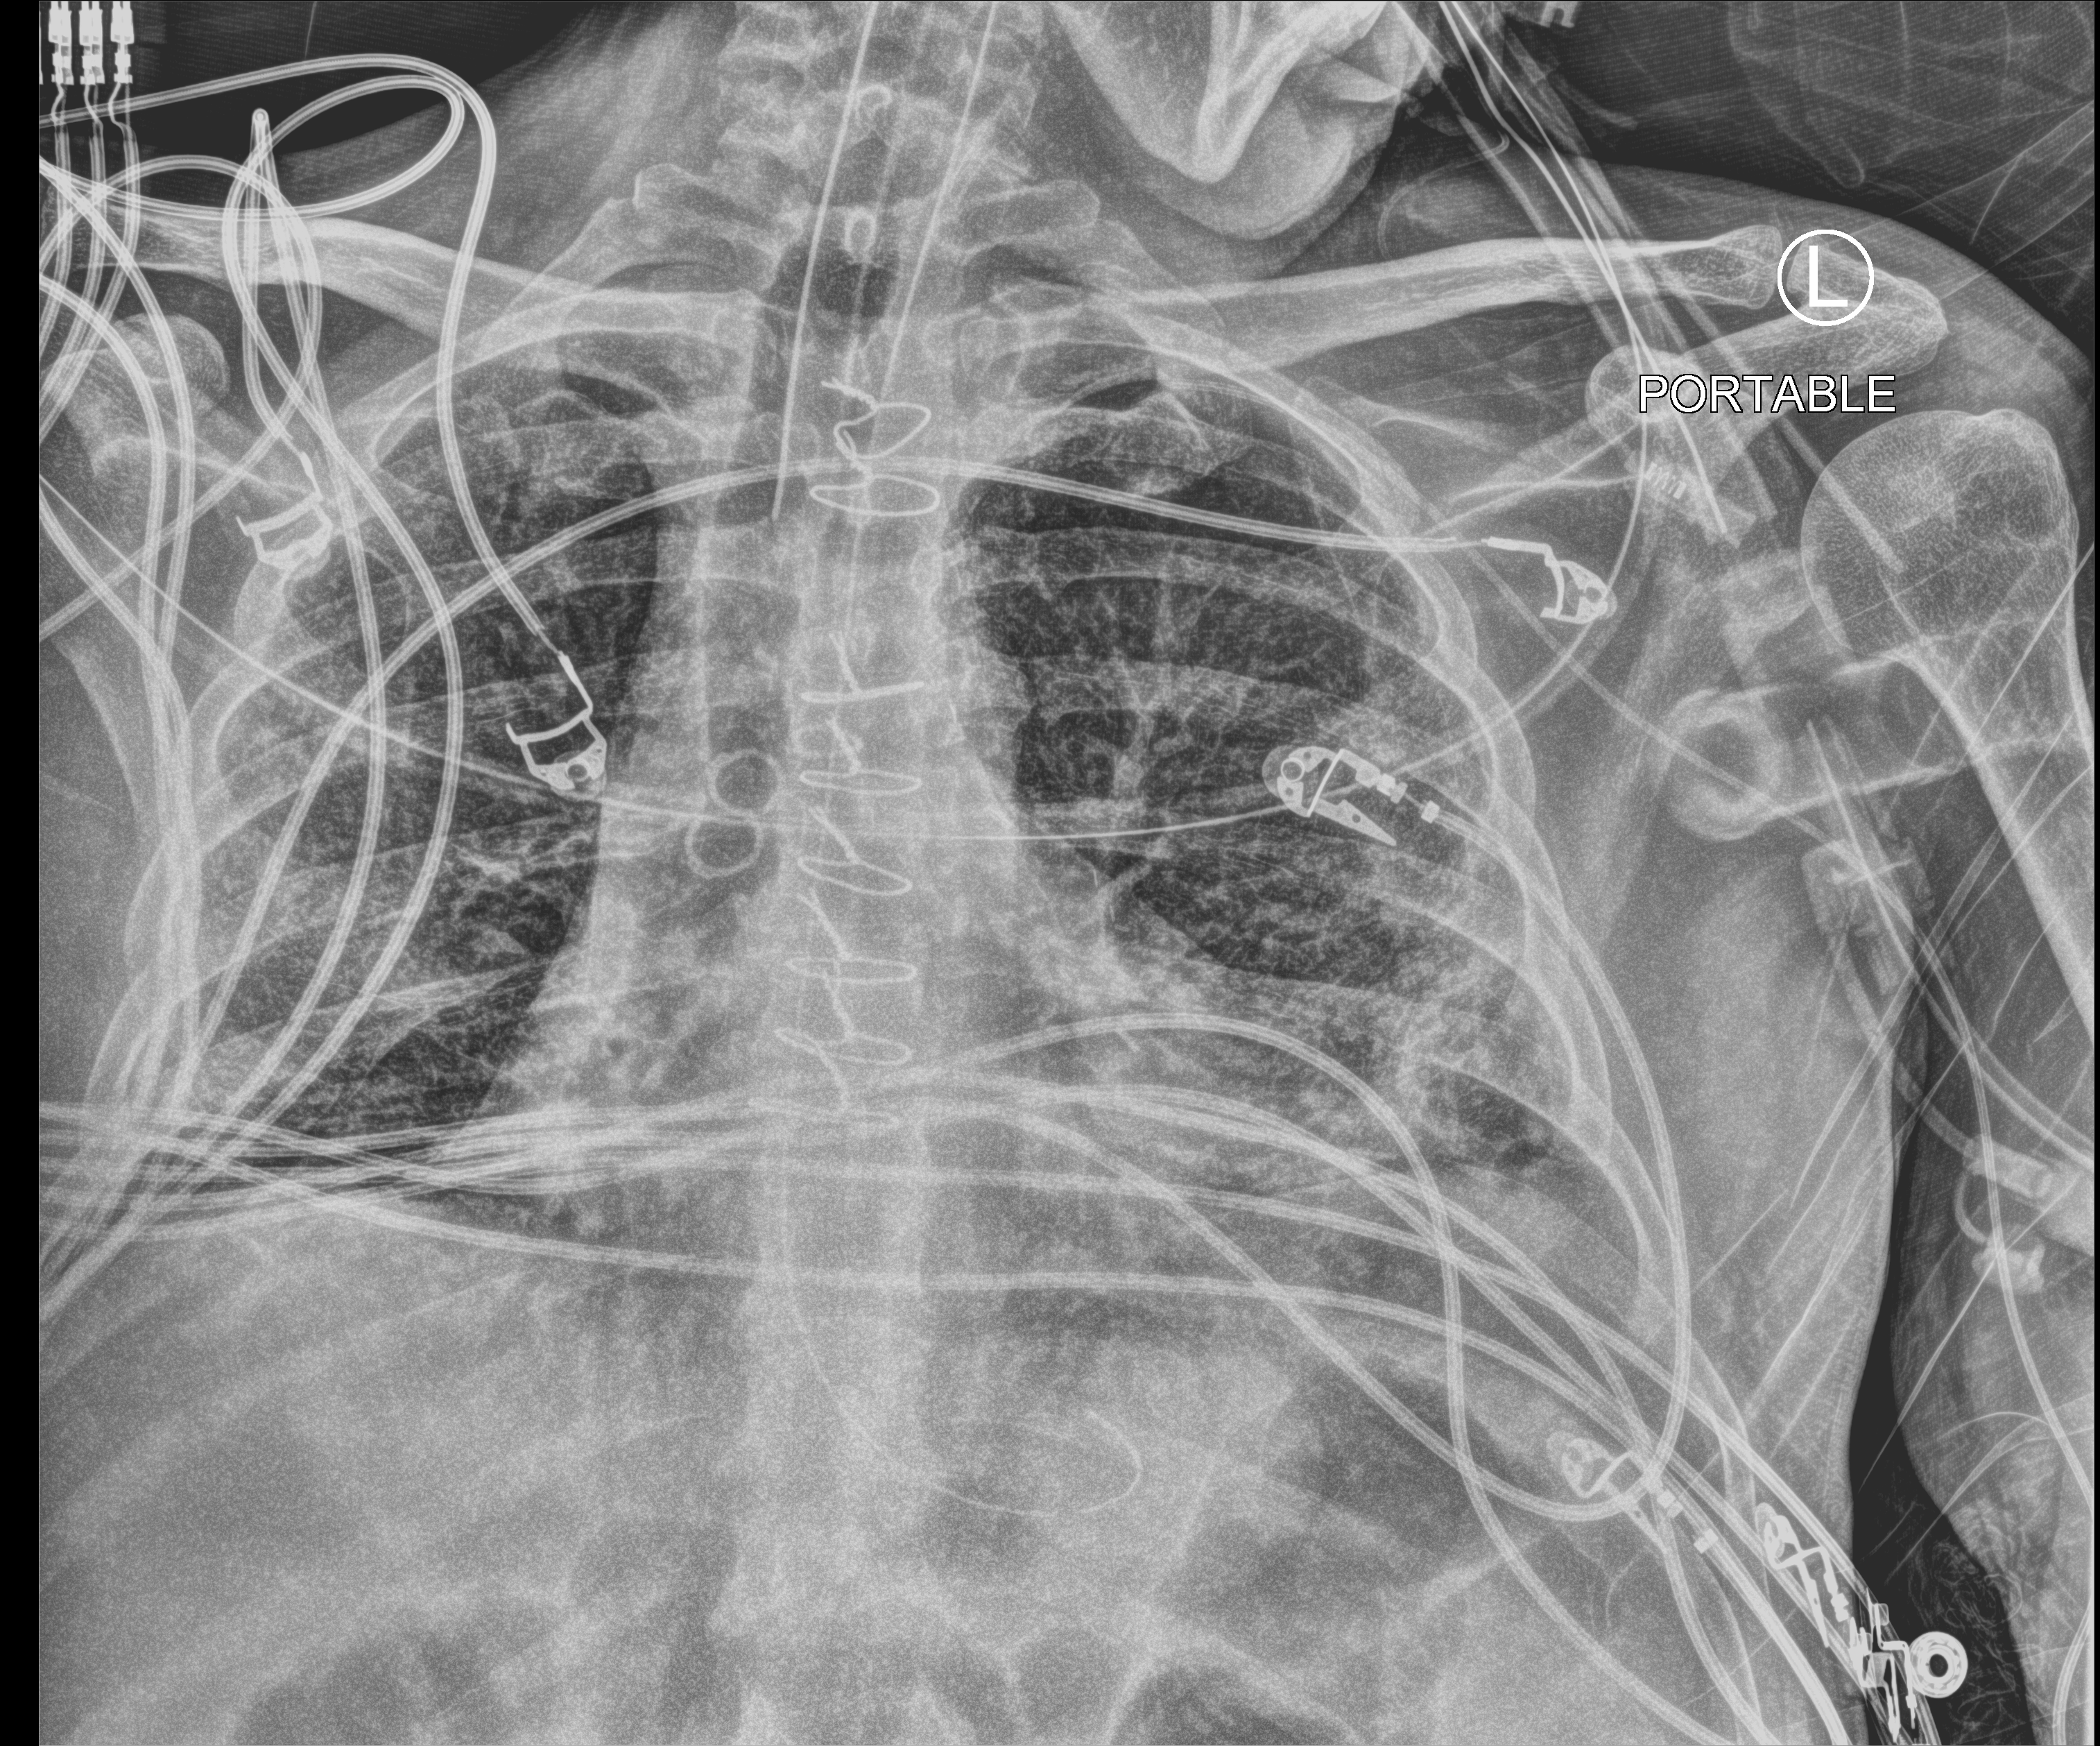
Portable chest radiograph; anteroposterior (AP) projection. Patient hospitalised with COVID-19; male, aged 18–59 years.
From the hospital-stay record, not from the radiograph (when in the stay this image was taken is not recorded): chronic kidney disease (admission record): no; diabetes (admission record): yes; length of hospital stay: 63 days.